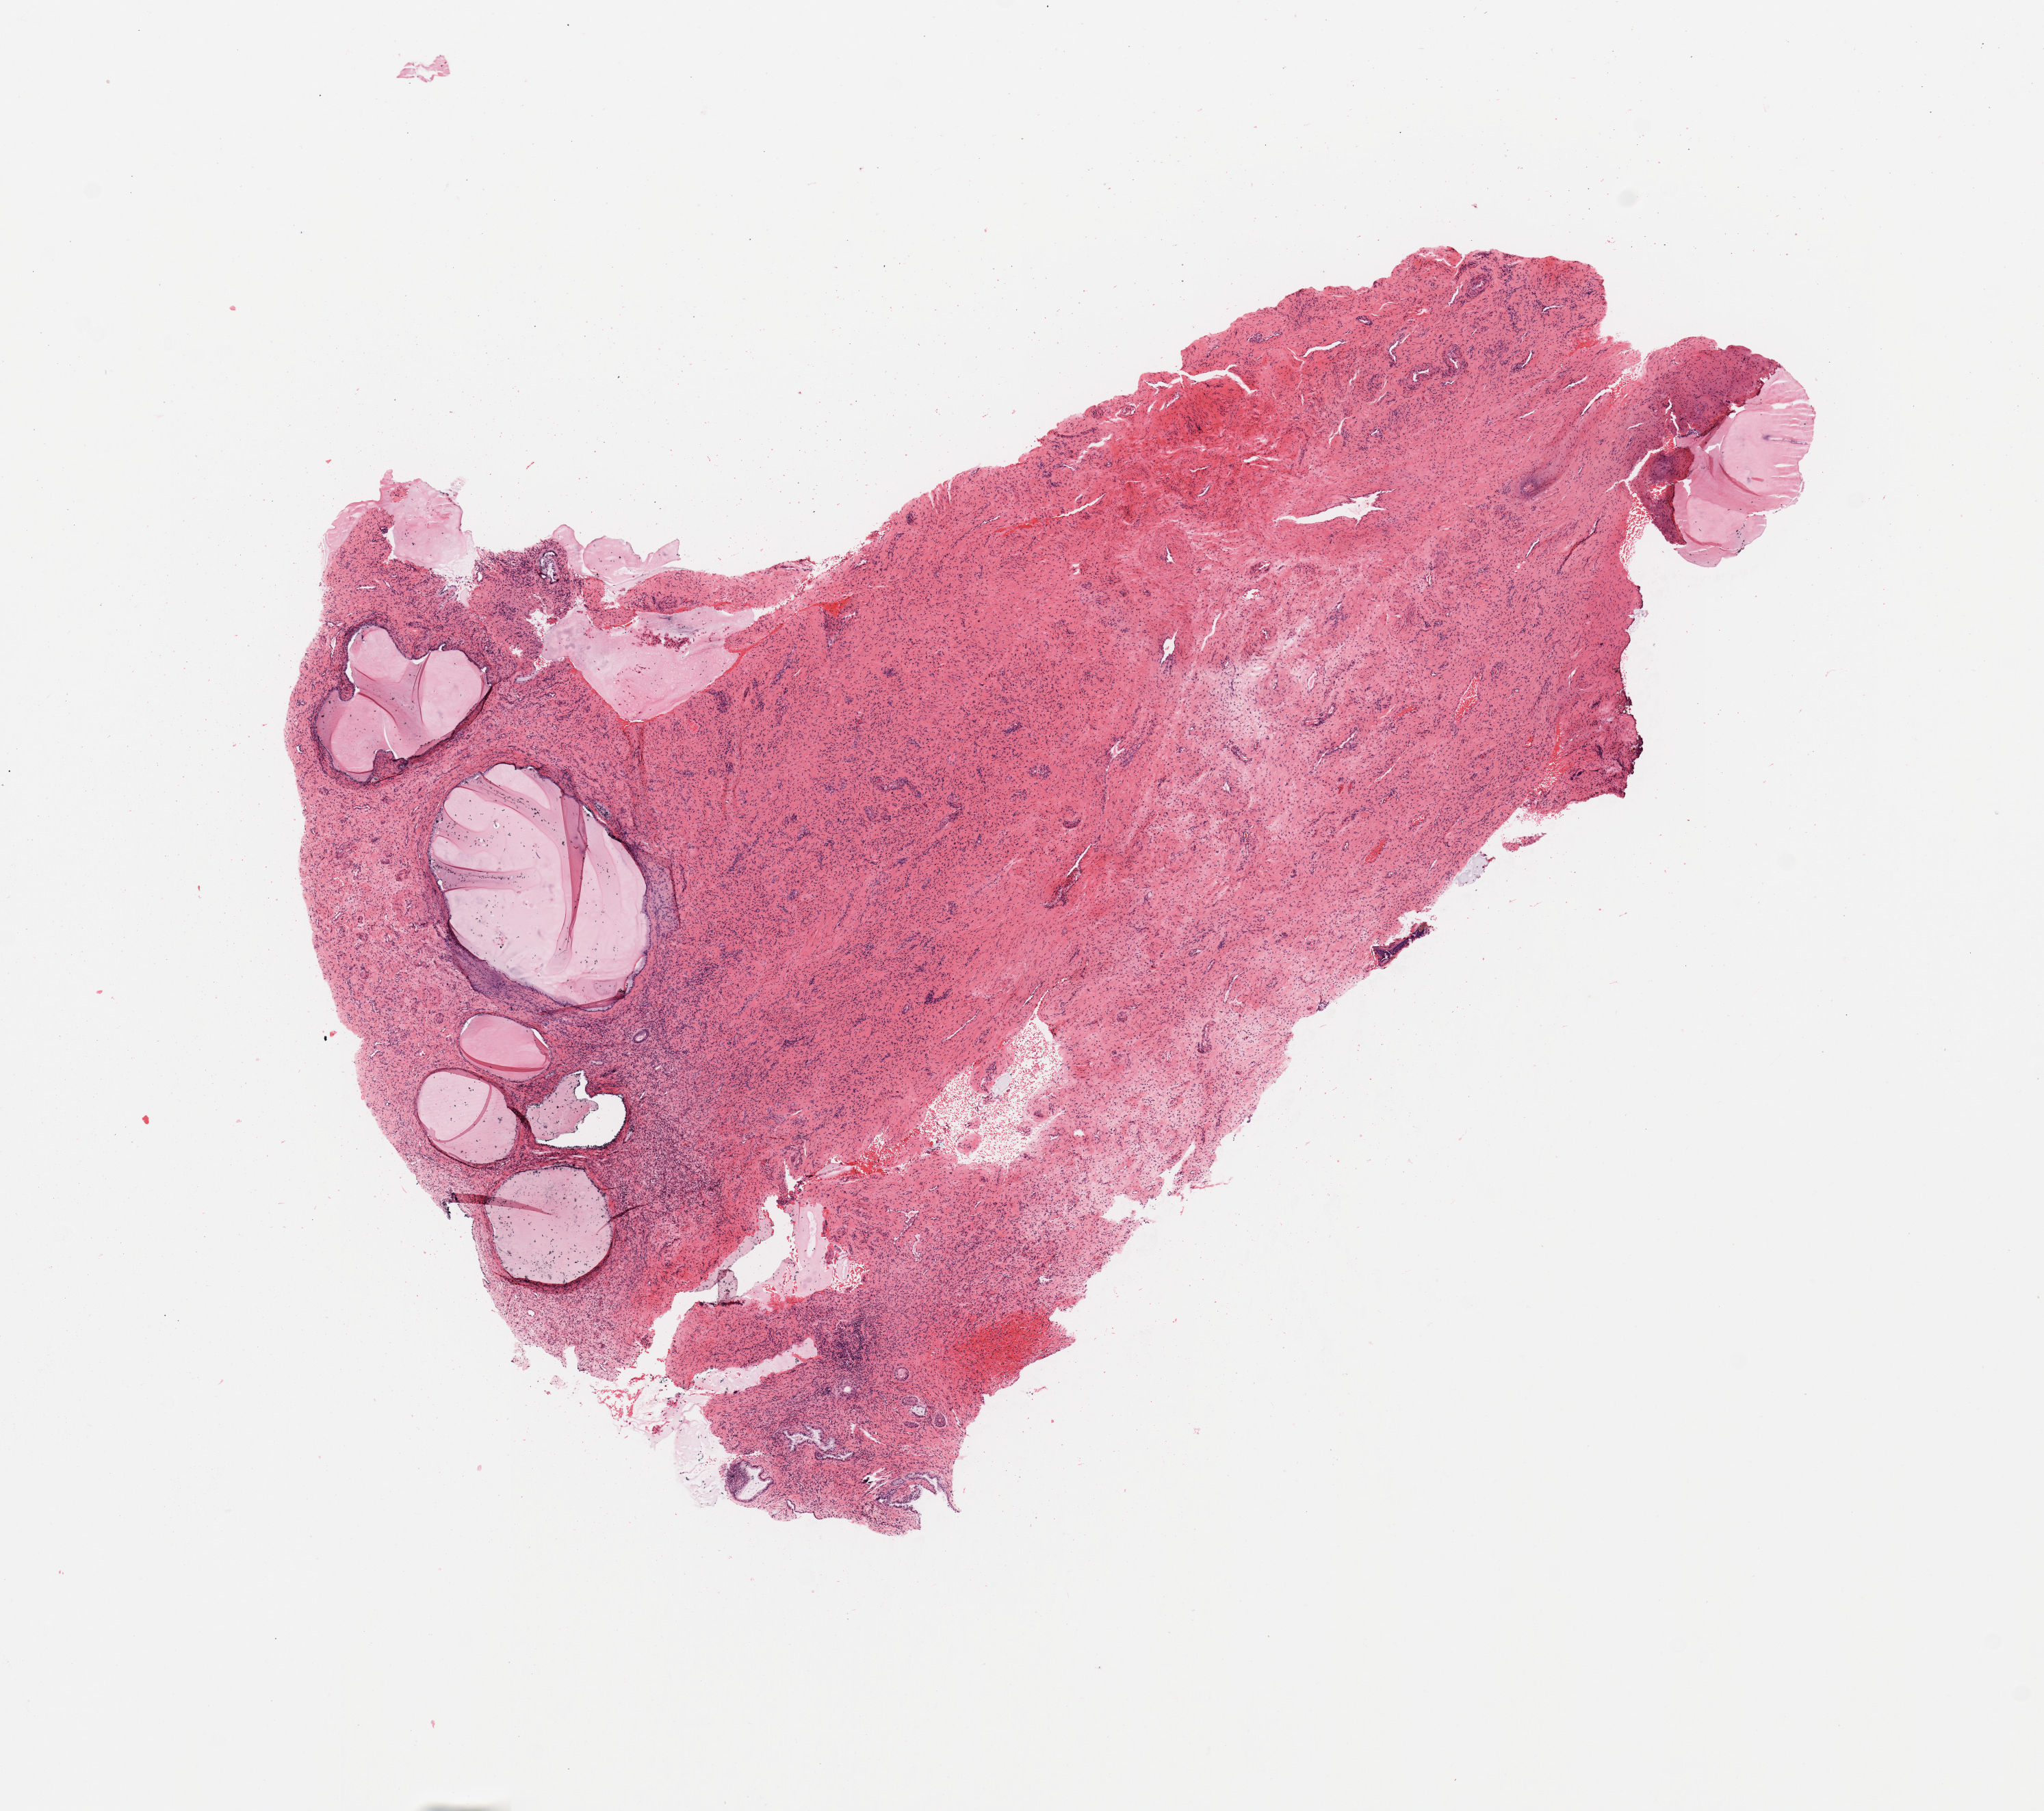
Whole-slide histology image, H&E — whole scanned area (about 11.8 x 10.5 mm, slide scanned at 20x) shown as a low-resolution overview; normal (non-tumour) tissue sample, sampled site: uterus. 60-year-old female patient.
This section: normal (non-tumour) tissue from the same patient. Patient diagnosis: Endometrioid adenocarcinoma, NOS.